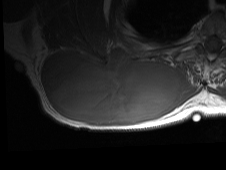
MRI of an extremity soft-tissue mass, one axial slice; slice 35 of 81 in the series (ordered by position); MR volume resampled by the dataset authors to the PET/CT grid (not the native acquisition matrix); 3.27 mm slice thickness; 226 × 170 image matrix. Male patient. Case-level facts recorded for this patient, not image findings: histological type: pleiomorphic spindle cell undifferentiated; grade: high; site of the primary tumour: right parascapusular.
Structures marked on this image (expert contour drawn on MRI and transferred to this co-registered scan by the dataset authors):
- gross tumour volume including surrounding oedema: box from (x=39, y=51) to (x=198, y=126) px
- gross tumour volume (mass): (x=39, y=51)–(x=180, y=125)